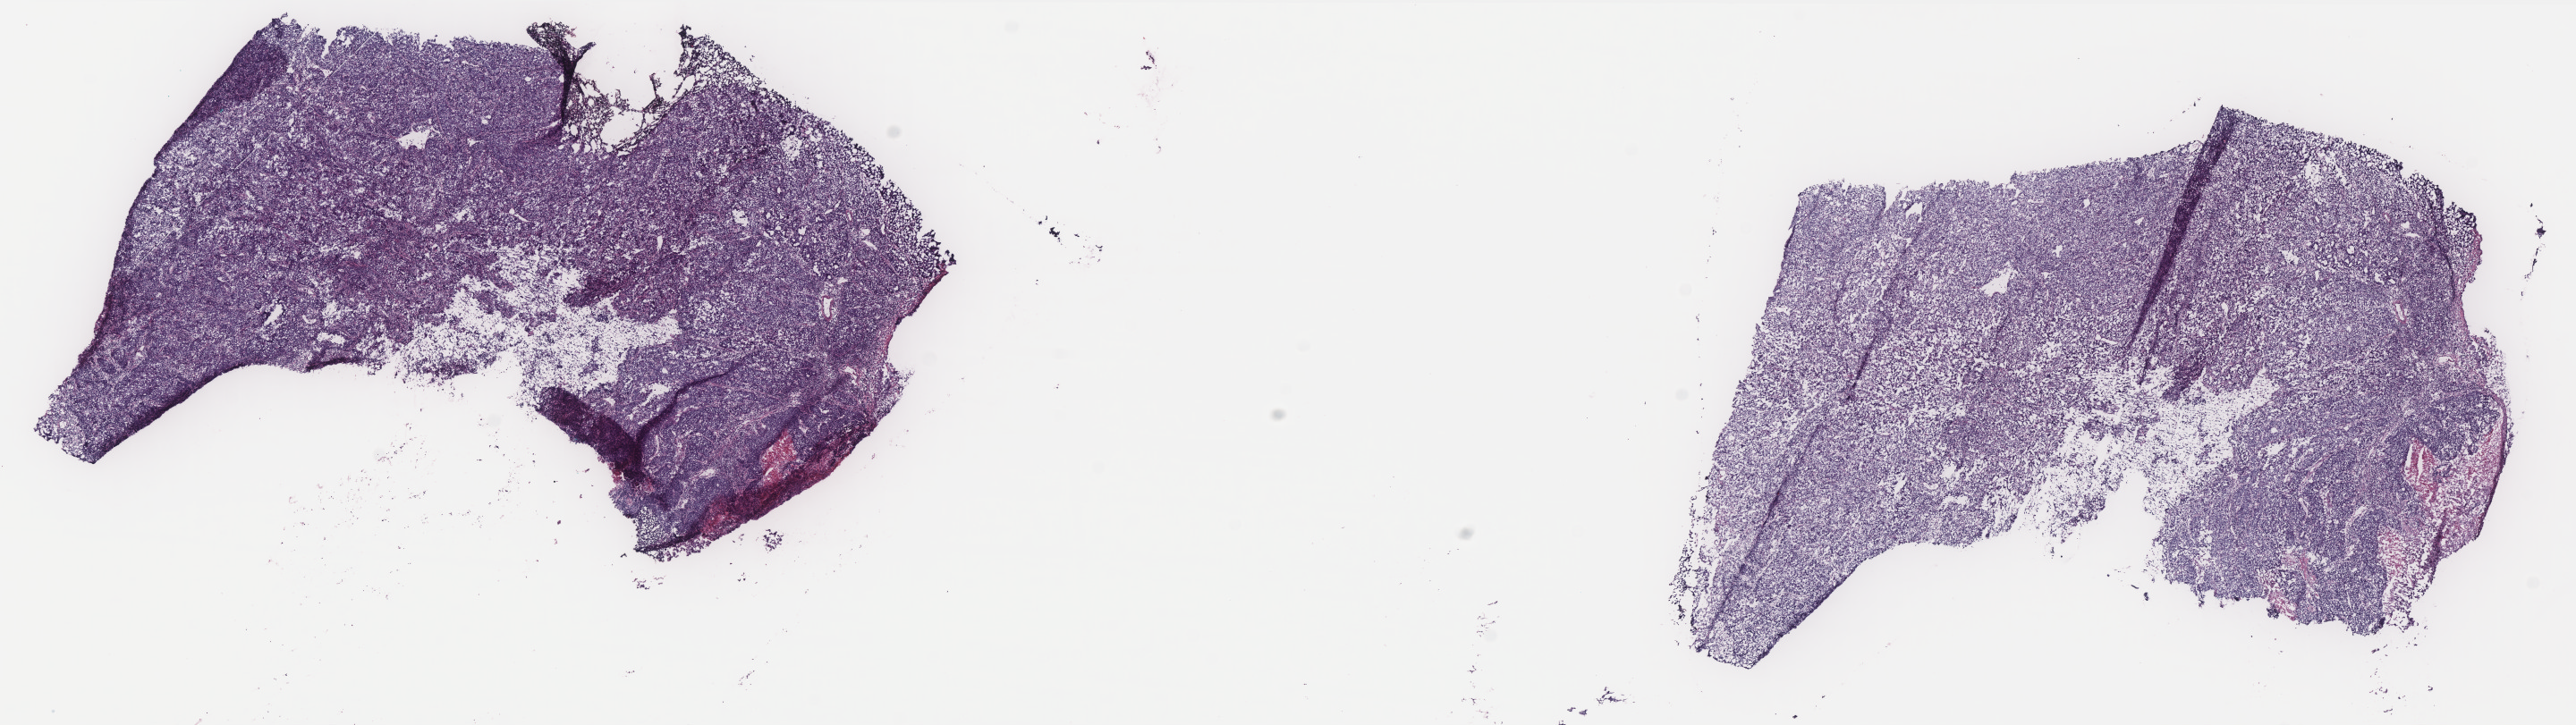
H&E-stained whole-slide image, shown as a low-resolution overview of the whole scanned area (about 23.1 x 6.5 mm). Frozen section. Uterus, primary tumour sample. Female, age 65 years at initial diagnosis. Histologic grade: G3 (poorly differentiated). Slide review estimates, as recorded: tumour cells 80%, tumour nuclei 90%, normal cells 0%, stromal cells 10%, necrosis 10%. Infiltration values recorded for this section: lymphocyte infiltration 6%, monocyte infiltration 0%, neutrophil infiltration 0%.
• FIGO stage: IB
• histologic diagnosis: Endometrioid adenocarcinoma, NOS (endometrium)